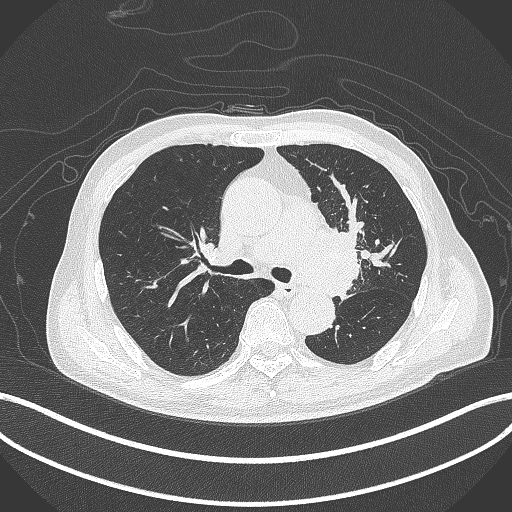
Chest CT, one axial slice. Position 272 of 417 along the scan axis. Reconstruction kernel B70f. 120 kVp. Lung window (W 1500 / L -600 HU). 1 mm slice thickness. 512 × 512 image matrix, field of view 400 × 400 mm. Patient: male, 77 years. Case-level facts recorded for this patient, not image findings: clinical TNM (as recorded): T3 N1 M0.
Structures marked on this image (bounding box drawn by a radiologist):
- lung tumour (recorded histology: adenocarcinoma): box from (x=316, y=221) to (x=369, y=299) px